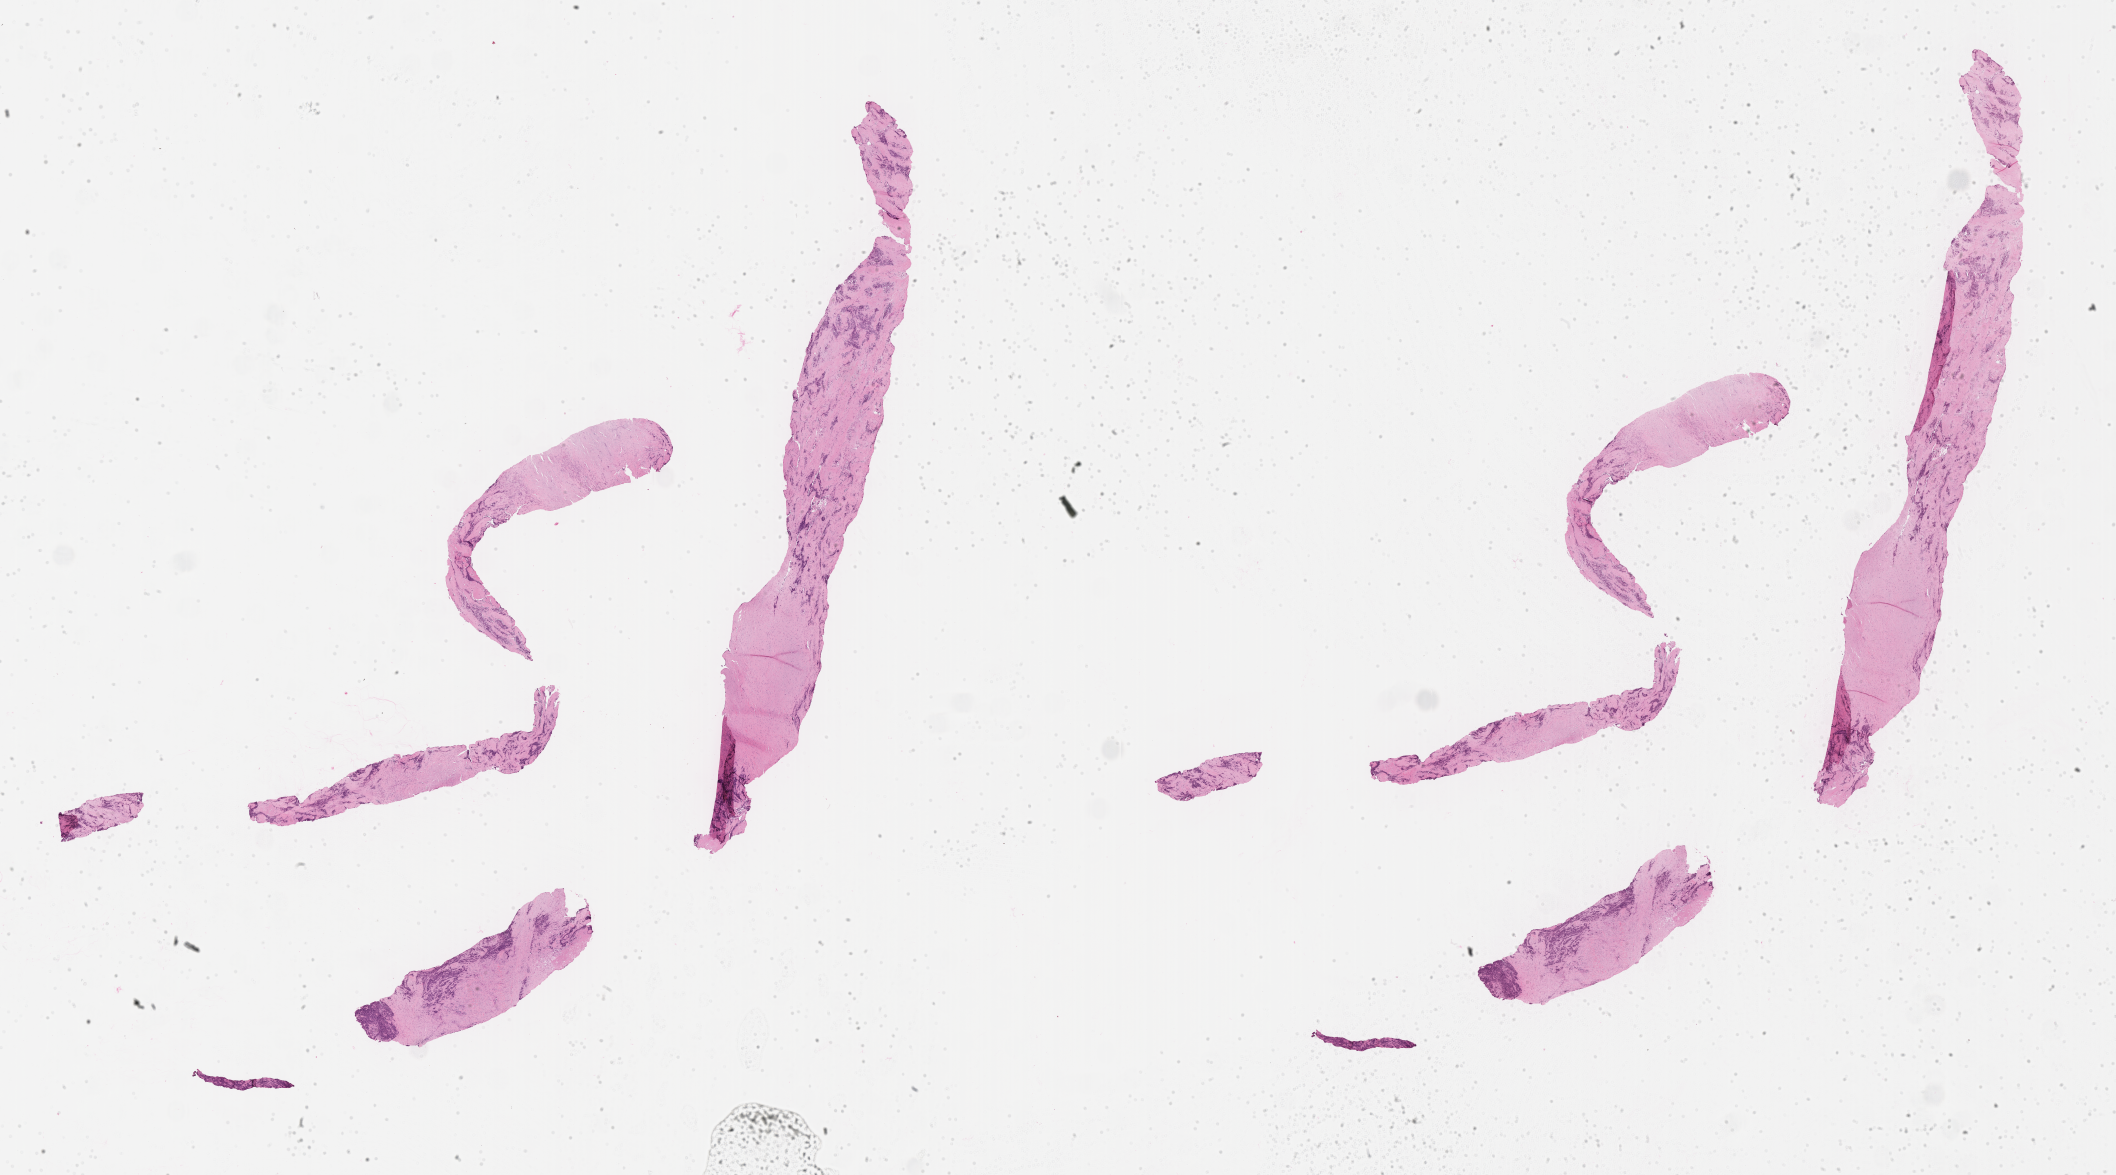
Digitized H&E-stained section of tumor tissue, low-resolution overview of the scanned area, about 34.2 x 19.0 mm. FFPE section. Sample anatomic site: soft tissue, thigh-right. Female patient, age at diagnosis 6.2 years.
Metastatic status at presentation (as recorded): metastatic (confirmed). Diagnosis: rhabdomyosarcoma; histological classification: alveolar rhabdomyosarcoma. Stage (as recorded): 4.